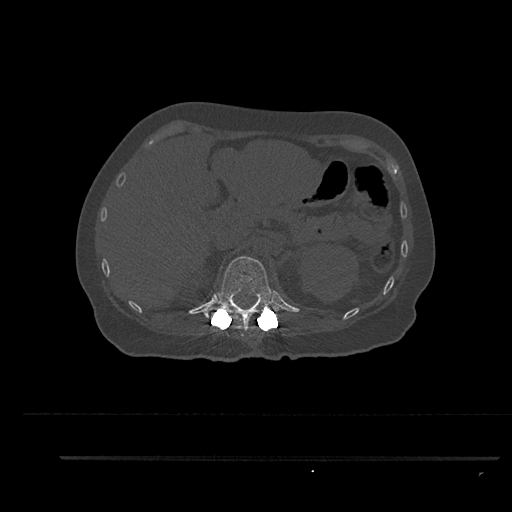
CT including the spine, one axial slice; position 263 of 797 along the scan axis; 120 kVp; bone window (W 1800 / L 400 HU); 0.5 mm slice thickness; 512 × 512 image matrix. Female patient, age 44 years. From the clinical record (not read from this slice): primary cancer: renal.
Outlined on this slice (semi-automatic segmentation, software-assisted and operator-edited):
- T12 vertebra: box from (x=205, y=256) to (x=281, y=332) px